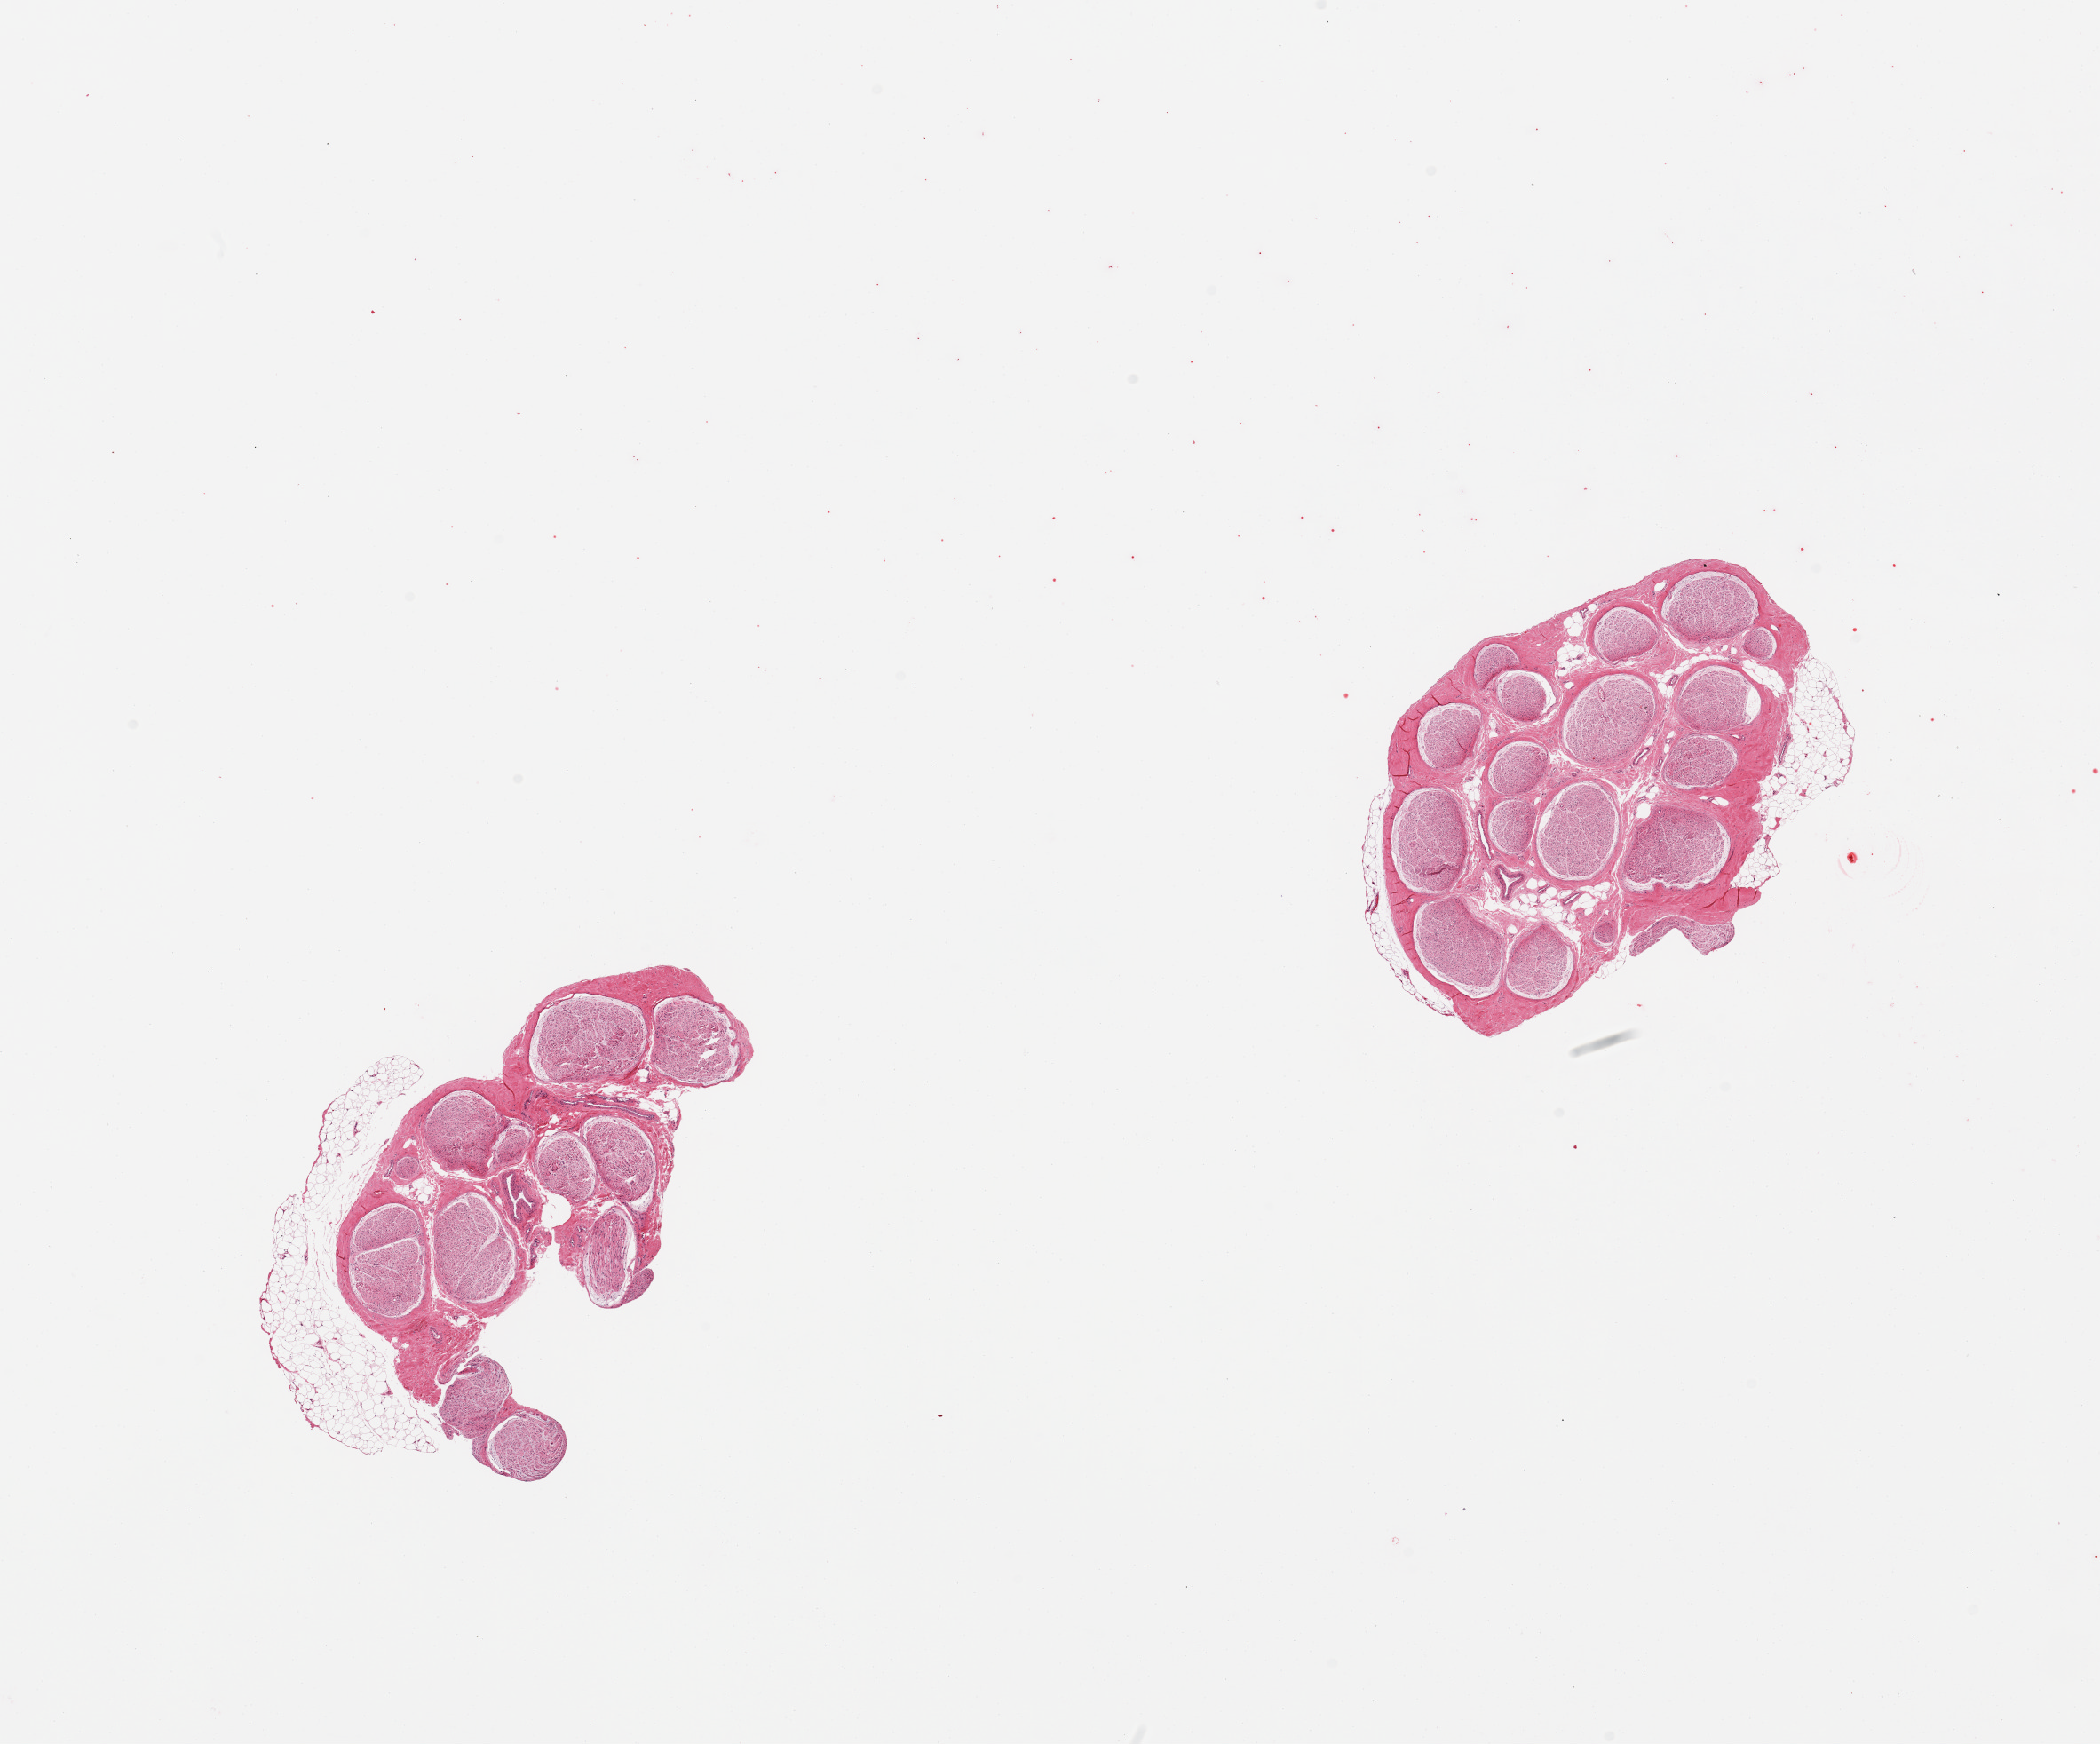
Whole-slide image, hematoxylin and eosin (H&E) stain — a low-resolution overview of the entire scanned area, about 18.7 x 15.5 mm (acquisition: 20x scan); PAXgene-fixed paraffin-embedded (PFPE) section; section of tibial nerve (target tissue); tissue donor sample. Donor sex: male.
Pathologist's review note for this sample: 2 pieces; up to 1mm of external fat.